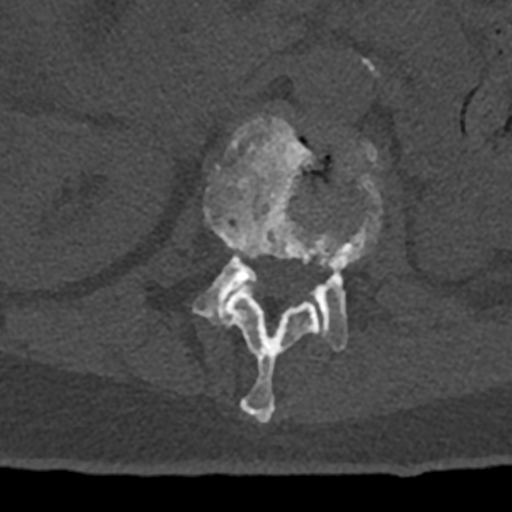
CT including the spine, one axial slice. Position 408 of 797 along the scan axis. Reconstruction kernel Br40s/3. Bone window (W 1800 / L 400 HU). 512 × 512 image matrix, field of view 160 × 160 mm. Patient: male, 74 years. From the clinical record (not read from this slice): primary cancer: renal.
Annotated regions visible in this slice (semi-automatic segmentation, software-assisted and operator-edited):
- L1 vertebra: bounding box [x1, y1, x2, y2] px = [203, 116, 339, 423]
- L2 vertebra: [192, 142, 382, 351]